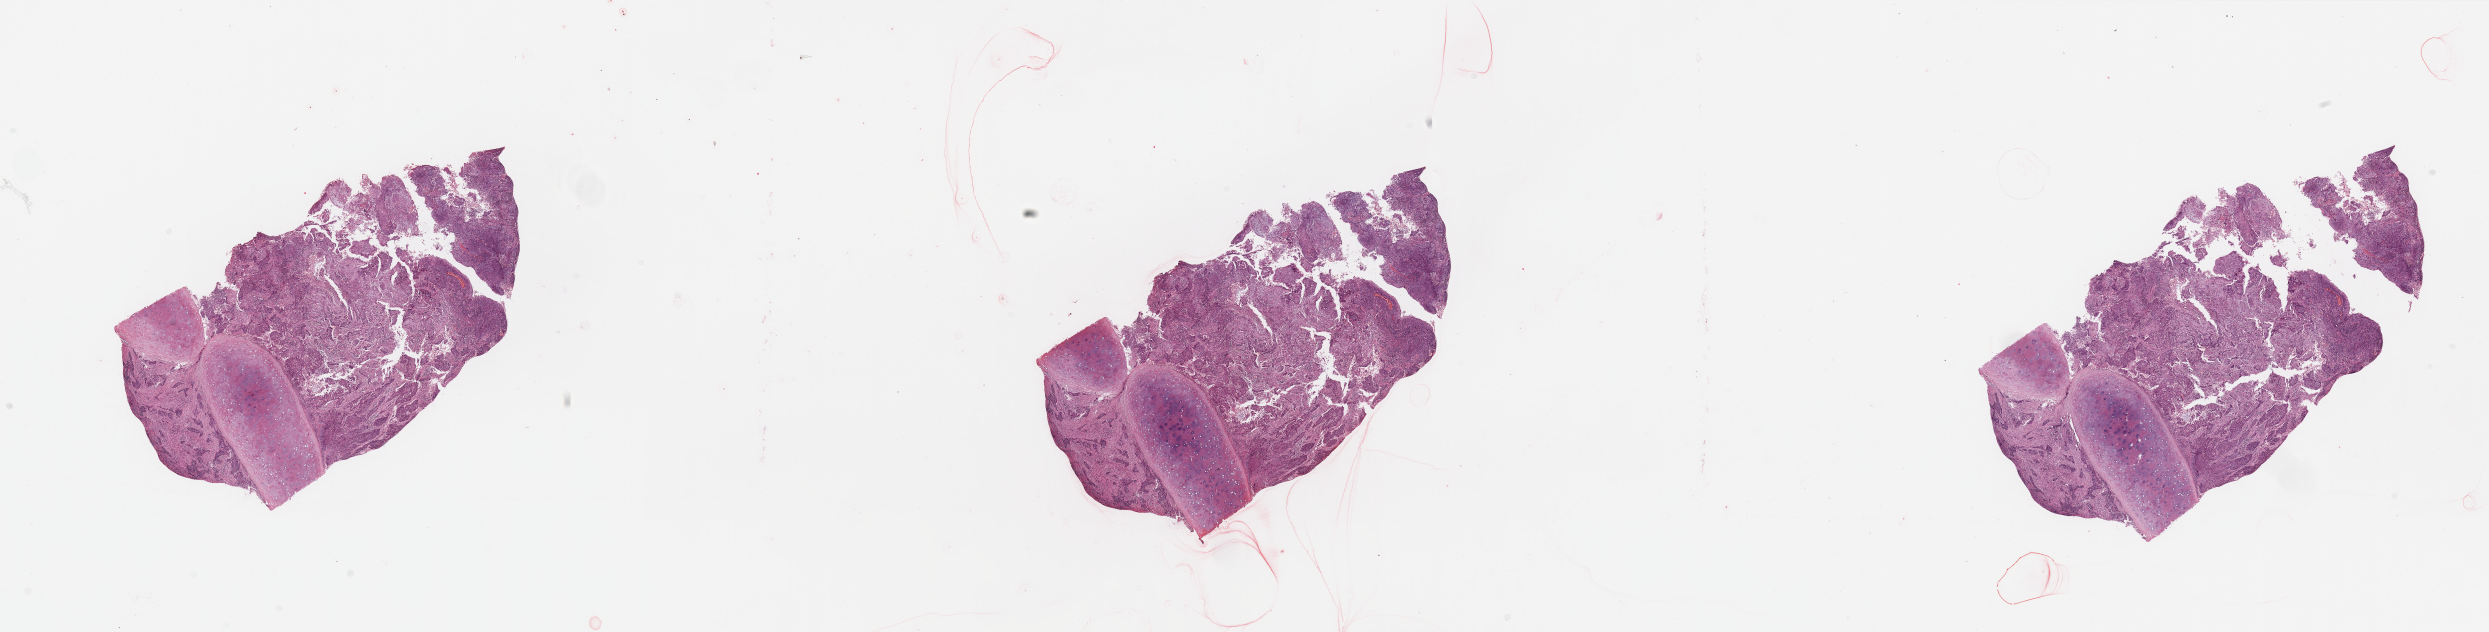
Whole-slide histology image, H&E-stained — whole scanned area (about 39.4 x 10.0 mm) shown as a low-resolution overview. Tumour tissue sample, sampled site: lung. Patient: male, age 73 years. Histologic grade: G2 (moderately differentiated). Composition of this section per pathologist review: tumour nuclei 60%, necrosis 5%.
Diagnosis: Squamous cell carcinoma, NOS. Primary tumour site (as recorded): right middle lobe. AJCC pathologic stage: II.